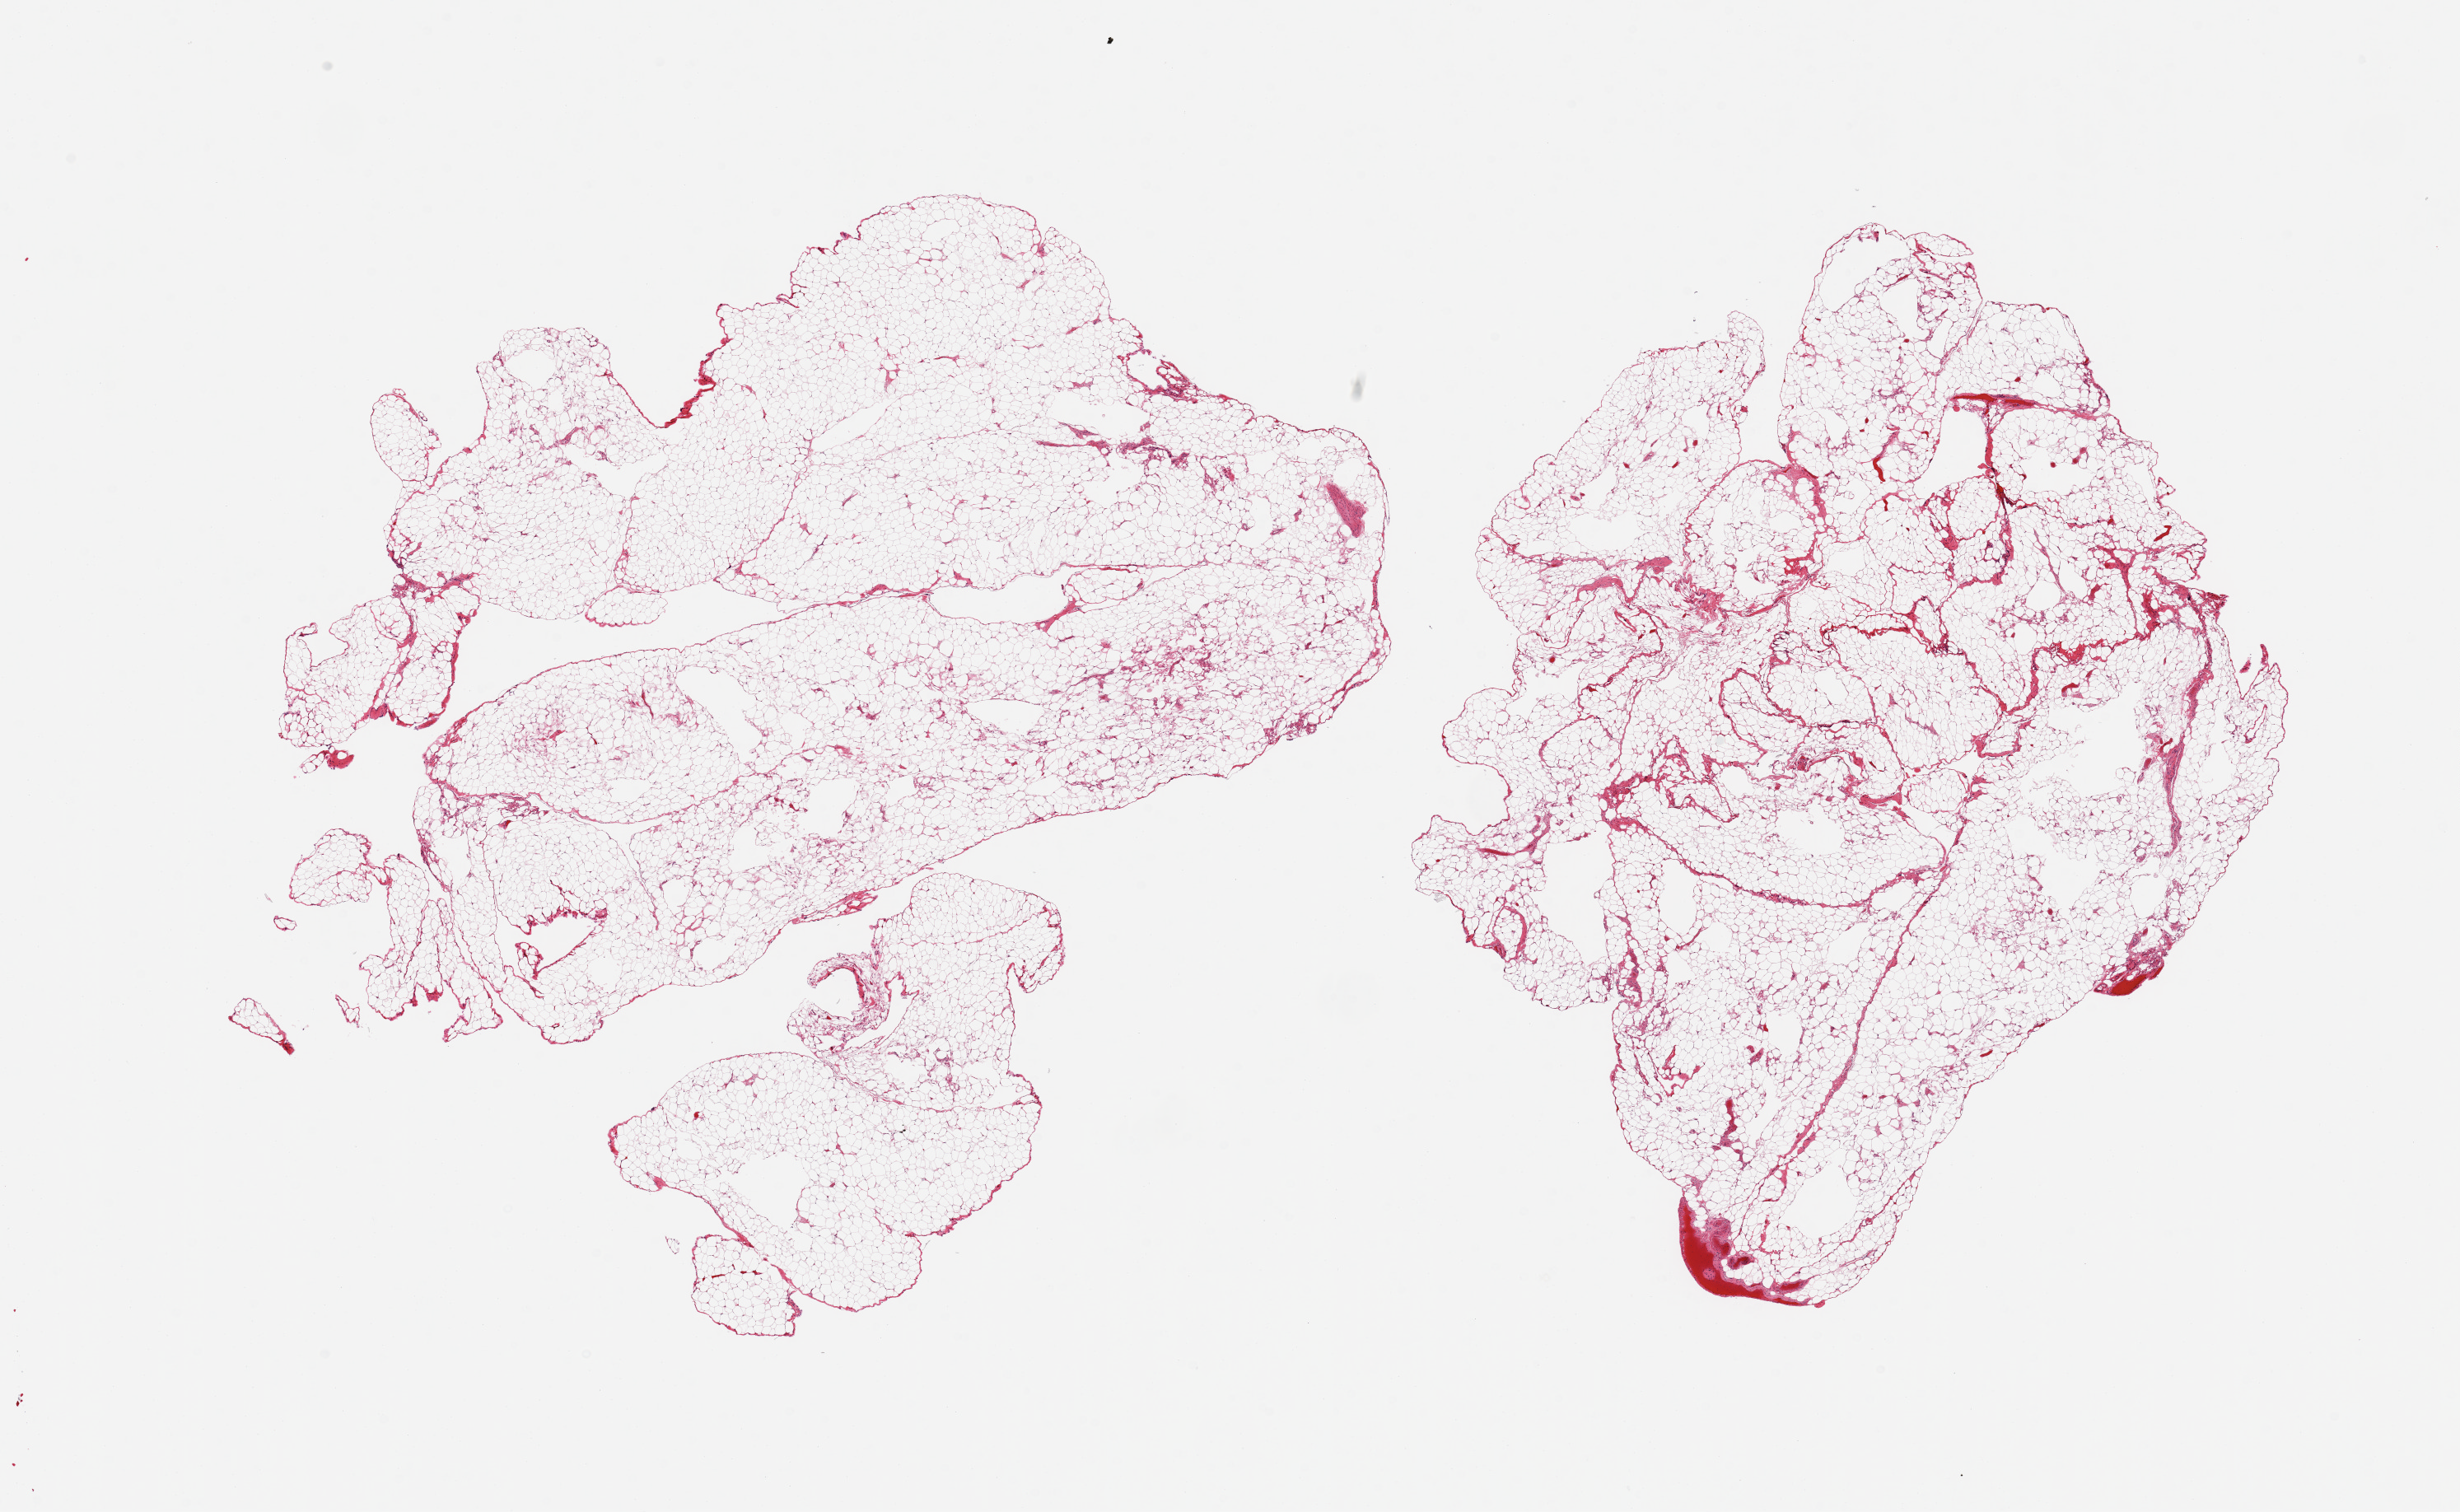
Whole-slide image, hematoxylin and eosin (H&E) stain, brightfield — whole scanned area (about 23.6 x 14.5 mm) shown as a low-resolution overview, PAXgene-fixed paraffin-embedded (PFPE) section, sampled site (target tissue): omentum, tissue donor sample.
- reviewer comment on this tissue sample: 2 pieces trace fascia/vascular elements